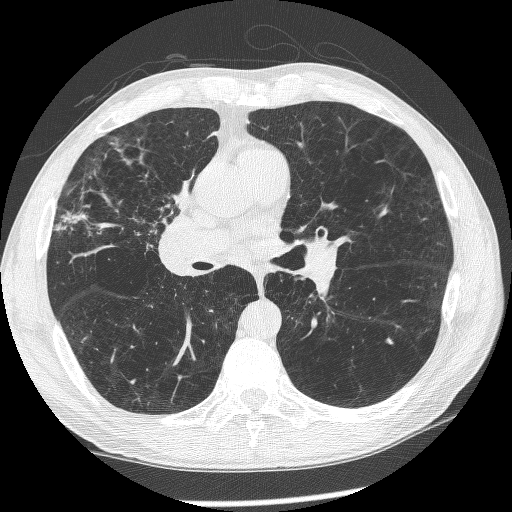
Chest CT (low-dose screening protocol), one axial image. First (baseline) screen. Lung window (W 1500 / L -600 HU). 1.25 mm slice thickness. 512 × 512 image matrix. Male participant, aged 60 years at enrolment. Current smoker at enrolment.
• Expert-annotated lung lesion, bounding box [x1, y1, x2, y2] px = [145, 171, 214, 267].
• Screening reader's record for this exam (one nodule recorded; not confirmed to be the boxed lesion): non-calcified nodule or mass ≥4 mm, right upper lobe, 12 × 8 mm, spiculated (stellate) margins, mixed attenuation.
• Official screen result: positive, change unspecified: nodule(s) >= 4 mm or enlarging nodule(s), mass(es), or other non-specific abnormalities suspicious for lung cancer.
• Participant outcome: lung cancer diagnosed 208 days after this screen — squamous cell carcinoma, NOS, right upper lobe, right middle lobe, right main stem bronchus, poorly differentiated (G3), stage IV (AJCC 6th edition).